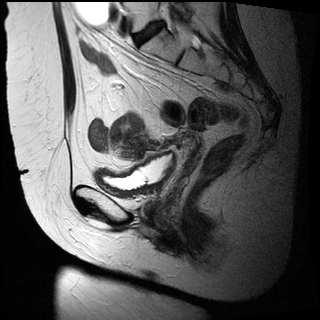
Pelvic MRI for cervical cancer, one sagittal slice; T2-weighted; 1.5 T; TE 89 ms, TR 2740 ms; 4 mm slice thickness; 320 × 320 image matrix. Female patient, age 47 years.
Structures marked on this image (expert manual segmentation):
- uterus and cervix: box from (x=124, y=137) to (x=151, y=160) px